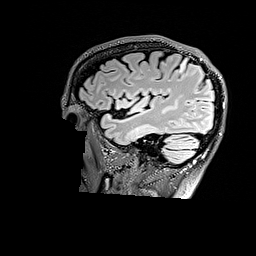
Brain MRI from a brain-tumour surgery series, one sagittal slice; slice 130 of 176 in the series (ordered by position); T2 FLAIR; 1 mm slice thickness; 256 × 256 image matrix, field of view 256 × 256 mm. From the clinical record (not read from this slice): histopathology: Astrocytoma; WHO grade: 3; IDH mutation: yes.
Outlined on this slice (outlined manually by an expert reader):
- tumour: bounding box [x1, y1, x2, y2] px = [179, 62, 186, 71]